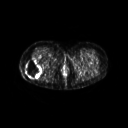
FDG PET of an extremity soft-tissue mass (from a PET/CT study), one axial slice. Slice 31 of 267 in the series (ordered by position). 128 × 128 image matrix, field of view 600 × 600 mm. Female patient, age 57 years. From the clinical record (not read from this slice): histological type: epithelioid sarcoma with vascular differentiation; site of the primary tumour: right buttock.
Annotated regions visible in this slice (expert contour drawn on MRI and transferred to this co-registered scan by the dataset authors):
- gross tumour volume (mass): bounding box (x1, y1, x2, y2) in pixels: (25, 59, 42, 78)